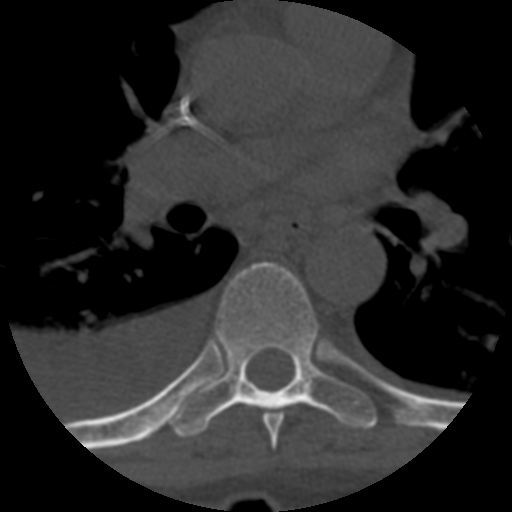
CT including the spine, one axial slice. Slice 421 of 708 in the series (ordered by position). One of 3 acquisitions stored at this slice position. Bone window (W 1800 / L 400 HU). 1.25 mm slice thickness. 512 × 512 image matrix, field of view 160 × 160 mm. Patient age 55 years. Case-level facts recorded for this patient, not image findings: primary cancer: colon; vertebrae with lytic lesions (as recorded): T12, L1, L5.
Structures marked on this image (semi-automatic segmentation, software-assisted and operator-edited):
- T6 vertebra: bounding box [x1, y1, x2, y2] px = [262, 411, 285, 450]
- T7 vertebra: [171, 262, 377, 438]